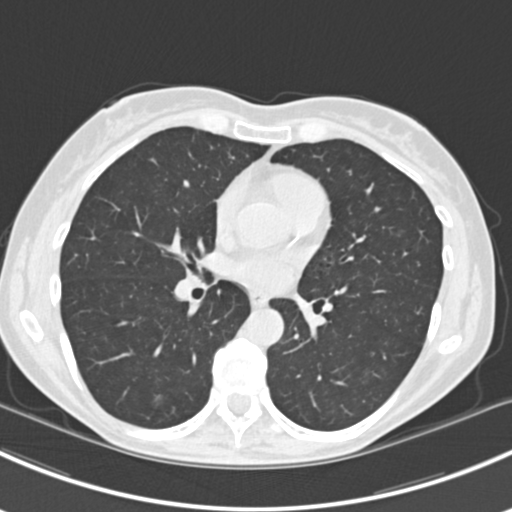
Axial slice from a low-dose chest CT screening exam; baseline annual screen; lung window (W 1500 / L -600 HU); 2 mm slice thickness. Female, age 63 years at enrolment. Current smoker at enrolment.
Lesion marked by an expert reader, bounding box [x1, y1, x2, y2] px = [376, 219, 423, 261]. The screening reader recorded 10 non-calcified nodules or masses ≥4 mm on this exam (right lower lobe, right lower lobe, left lower lobe, left lower lobe, right middle lobe, right lower lobe, left lower lobe, left upper lobe, right upper lobe, left upper lobe); which of them this box marks is not recorded. Lung cancer was diagnosed 751 days after this screen (after the third annual screen): bronchiolo-alveolar adenocarcinoma, NOS, right upper lobe, right middle lobe, right lower lobe, left upper lobe, left lower lobe, moderately differentiated (G2), stage IV (AJCC 6th edition).